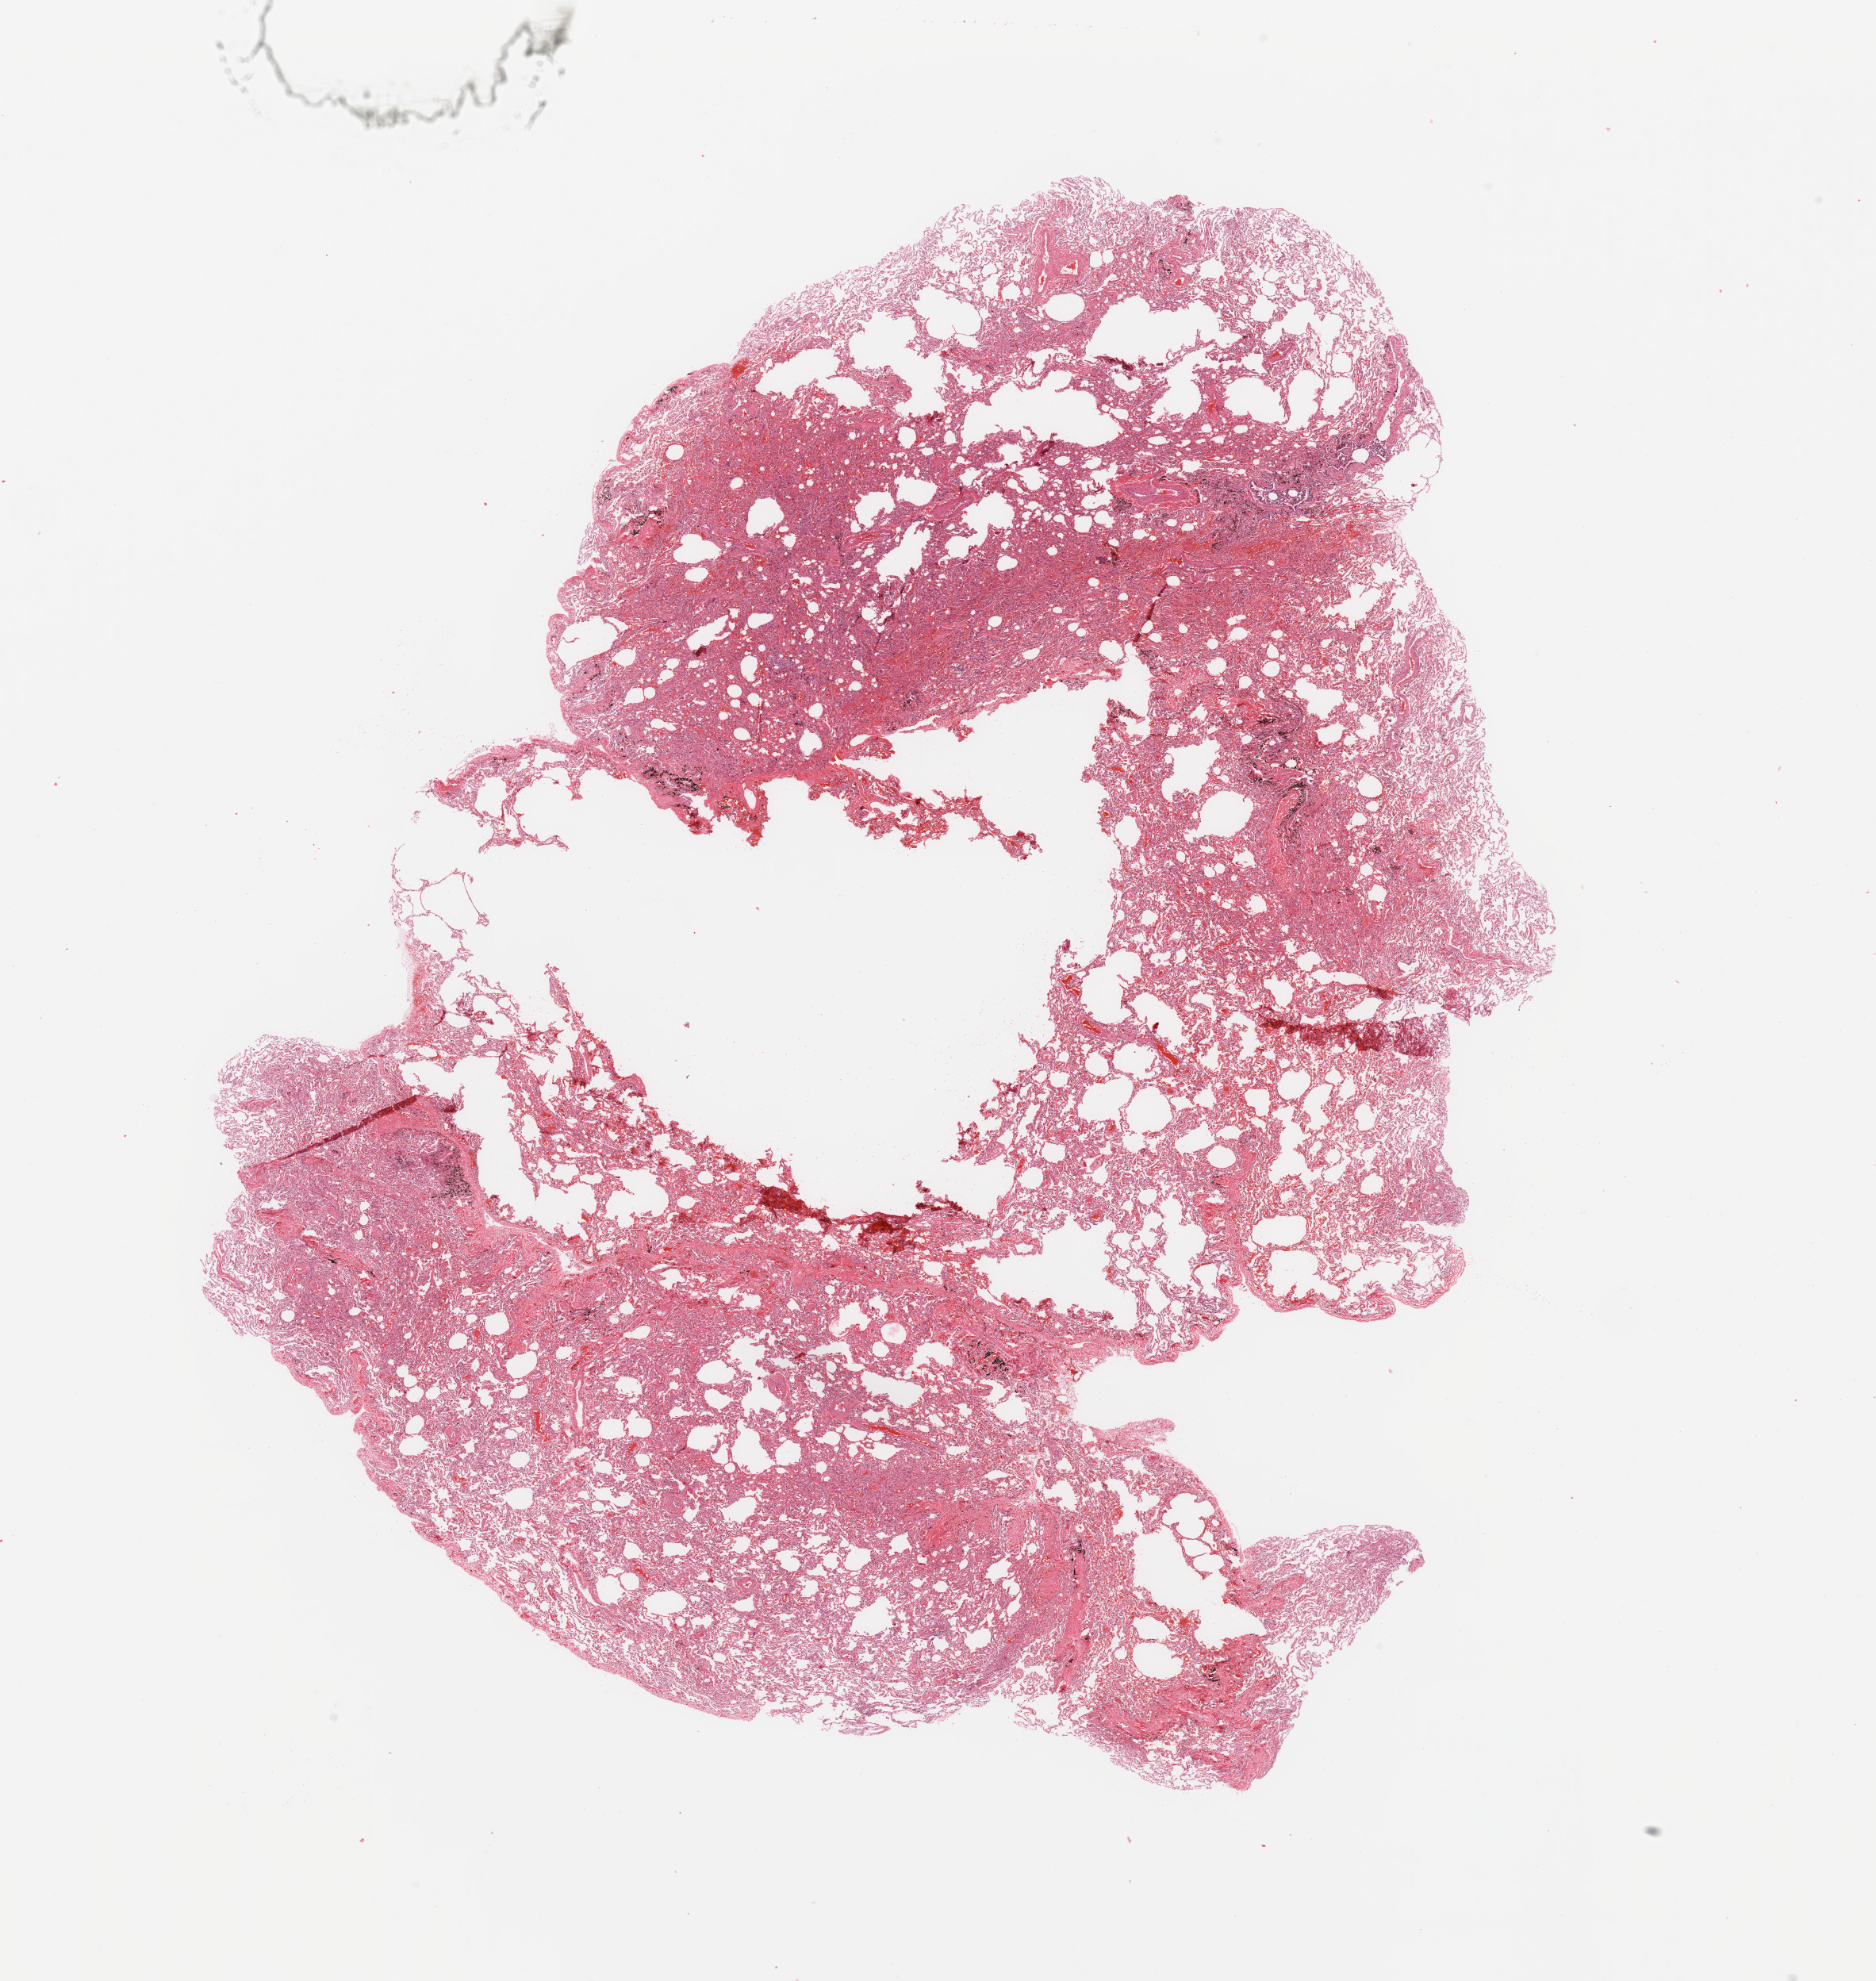
H&E whole-slide image, low-resolution overview of the scanned area, about 18.7 x 19.7 mm (slide scanned at 20x), normal (non-tumour) tissue sample, lung. 48-year-old male patient.
- this section: normal (non-tumour) tissue from the same patient
- patient diagnosis: Adenocarcinoma, NOS